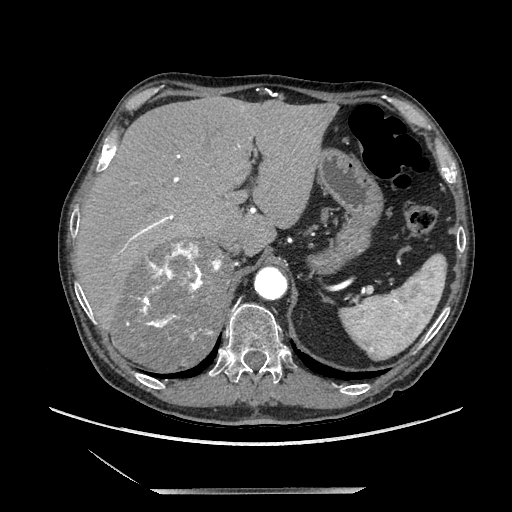
Contrast-enhanced abdominal CT, one axial slice. Position 156 of 243 along the scan axis. Soft-tissue window (W 400 / L 40 HU). 1.25 mm slice thickness. 512 × 512 image matrix, field of view 420 × 420 mm. Male patient. From the clinical record (not read from this slice): diagnosis: adrenocortical carcinoma; tumour side: right adrenal; tumour size at pathology: 16 cm; Ki-67 index: 17 %.
Annotated regions visible in this slice (semi-automatically segmented with operator editing):
- mass: bounding box <116,243,228,369> (left, top, right, bottom; pixels)